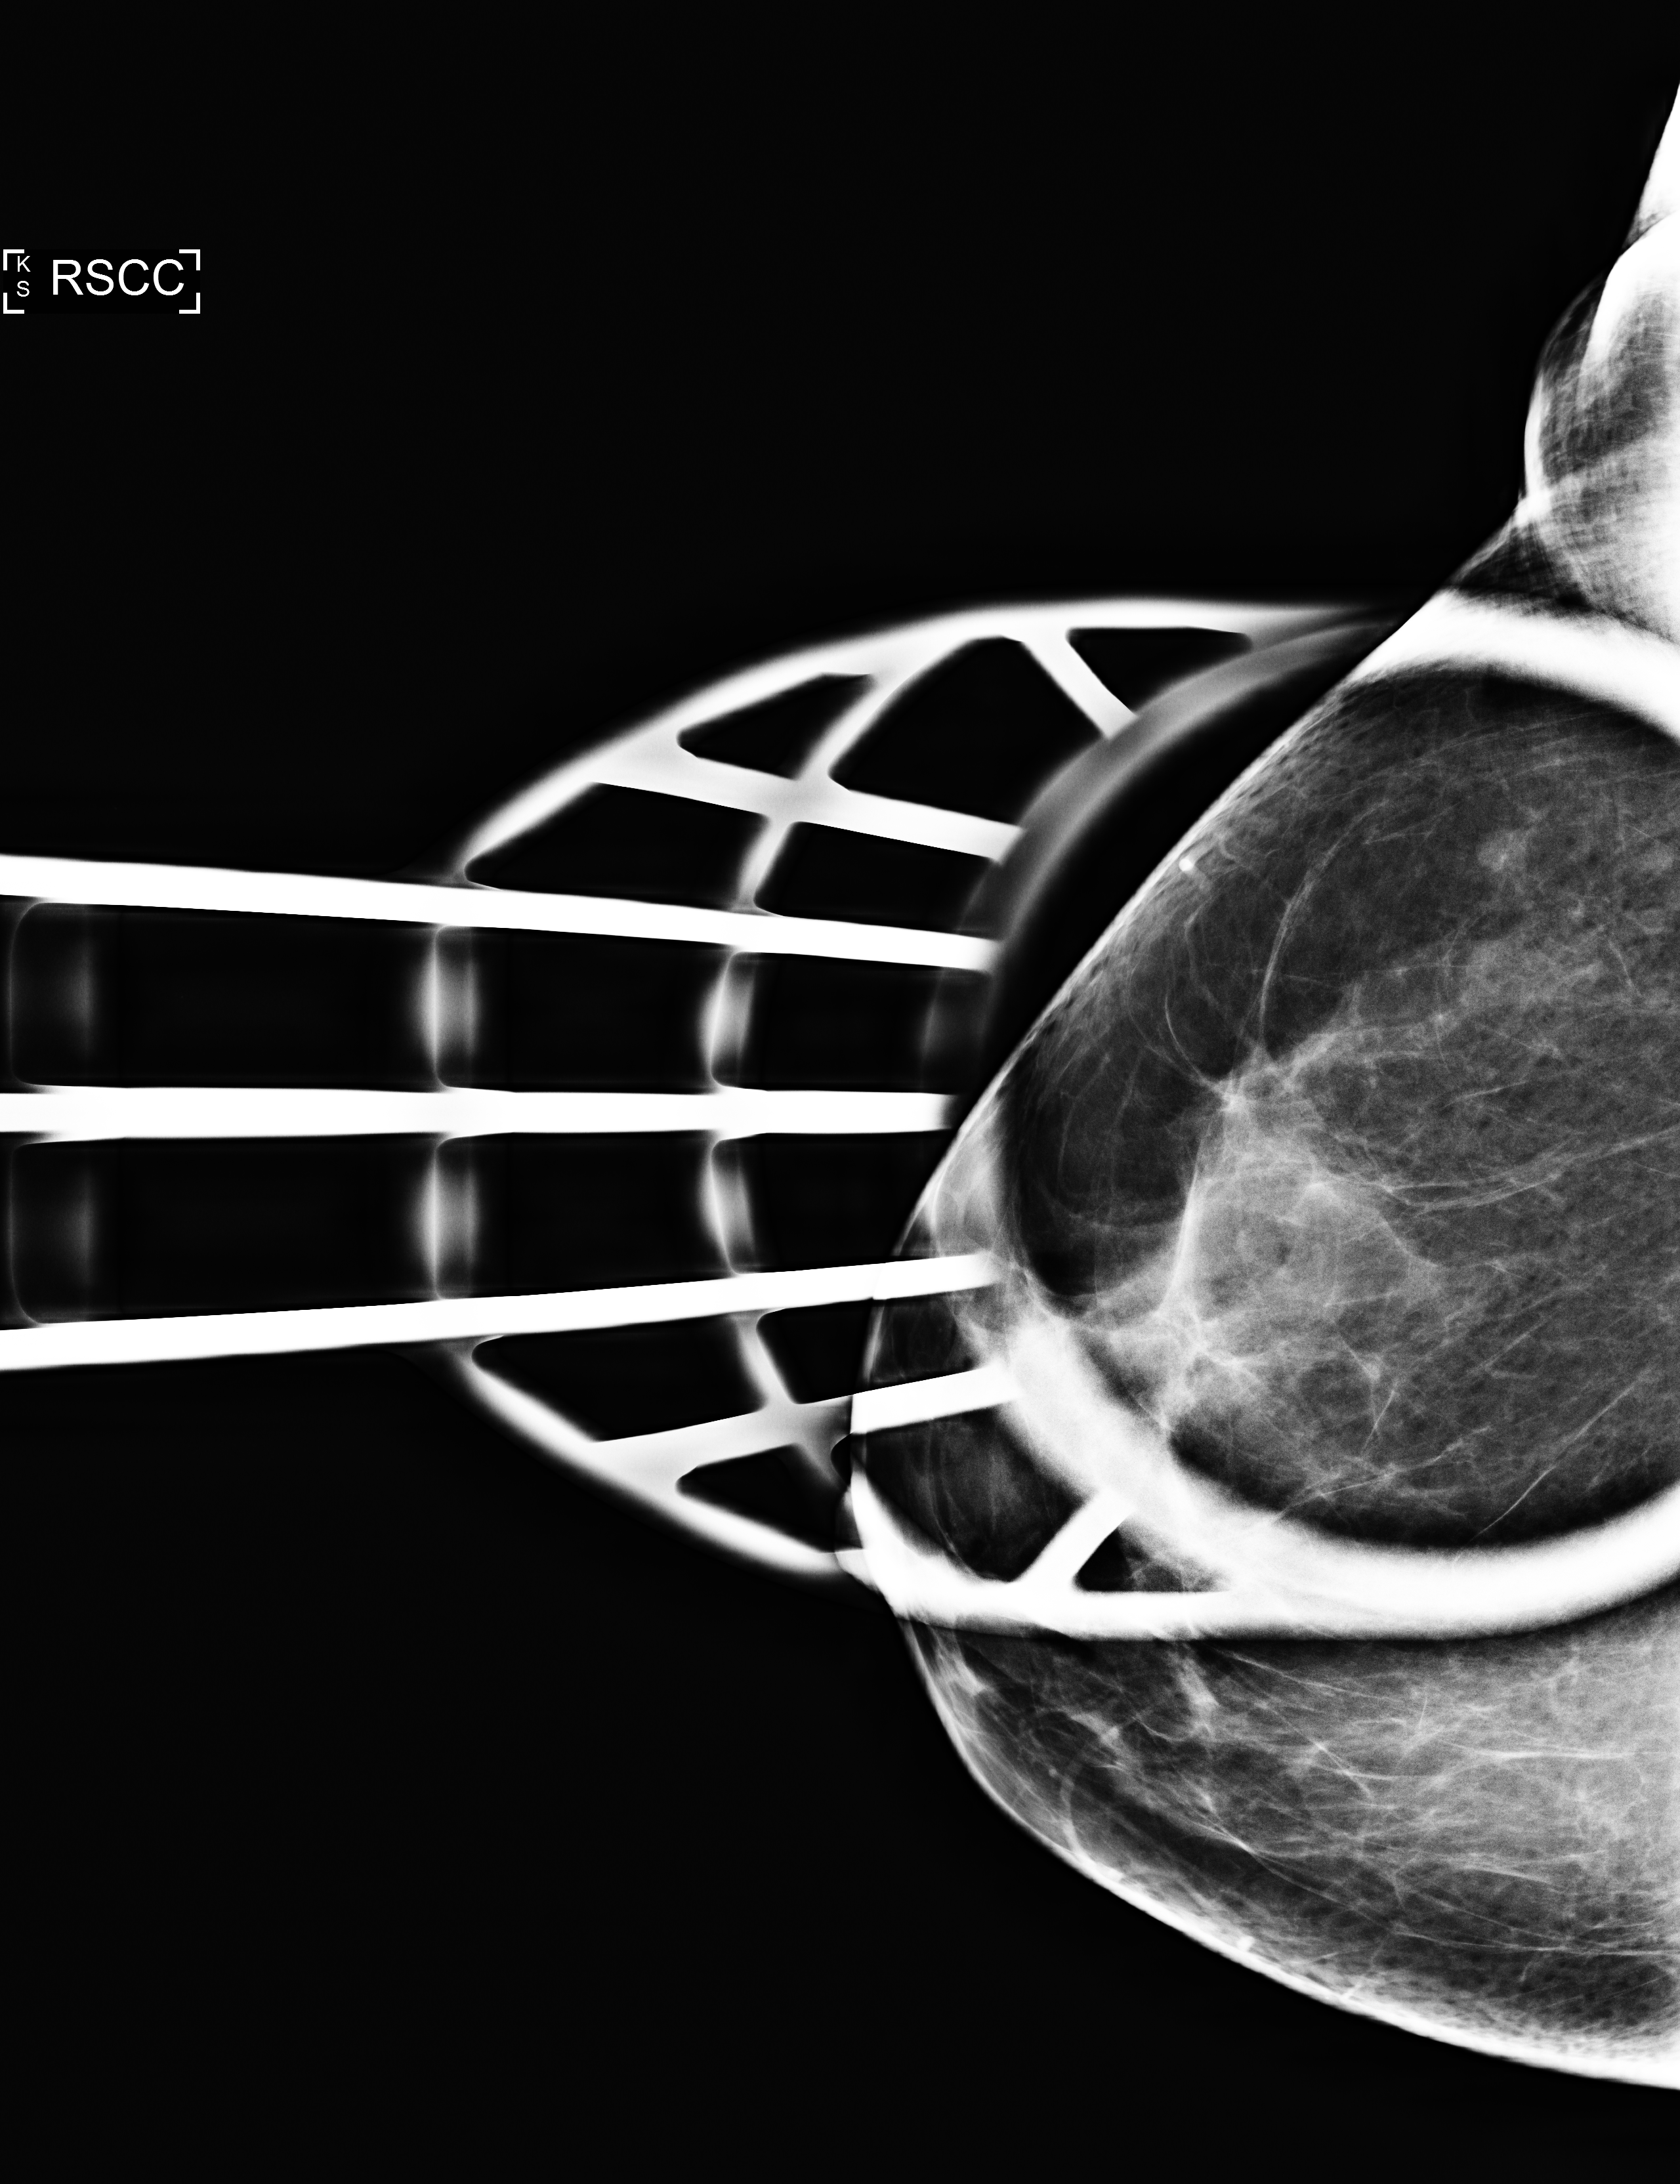
Digital mammogram (FFDM); right breast; craniocaudal (CC) view (spot compression); additional (diagnostic) view; system: Selenia Dimensions. Patient: female, 49 years.
Breast density at the screening exam (both breasts): heterogeneously dense (BI-RADS density category c). Final BI-RADS category for the screening round (tomosynthesis exam, both breasts): category 2. Recall: recalled for additional imaging after this screen.